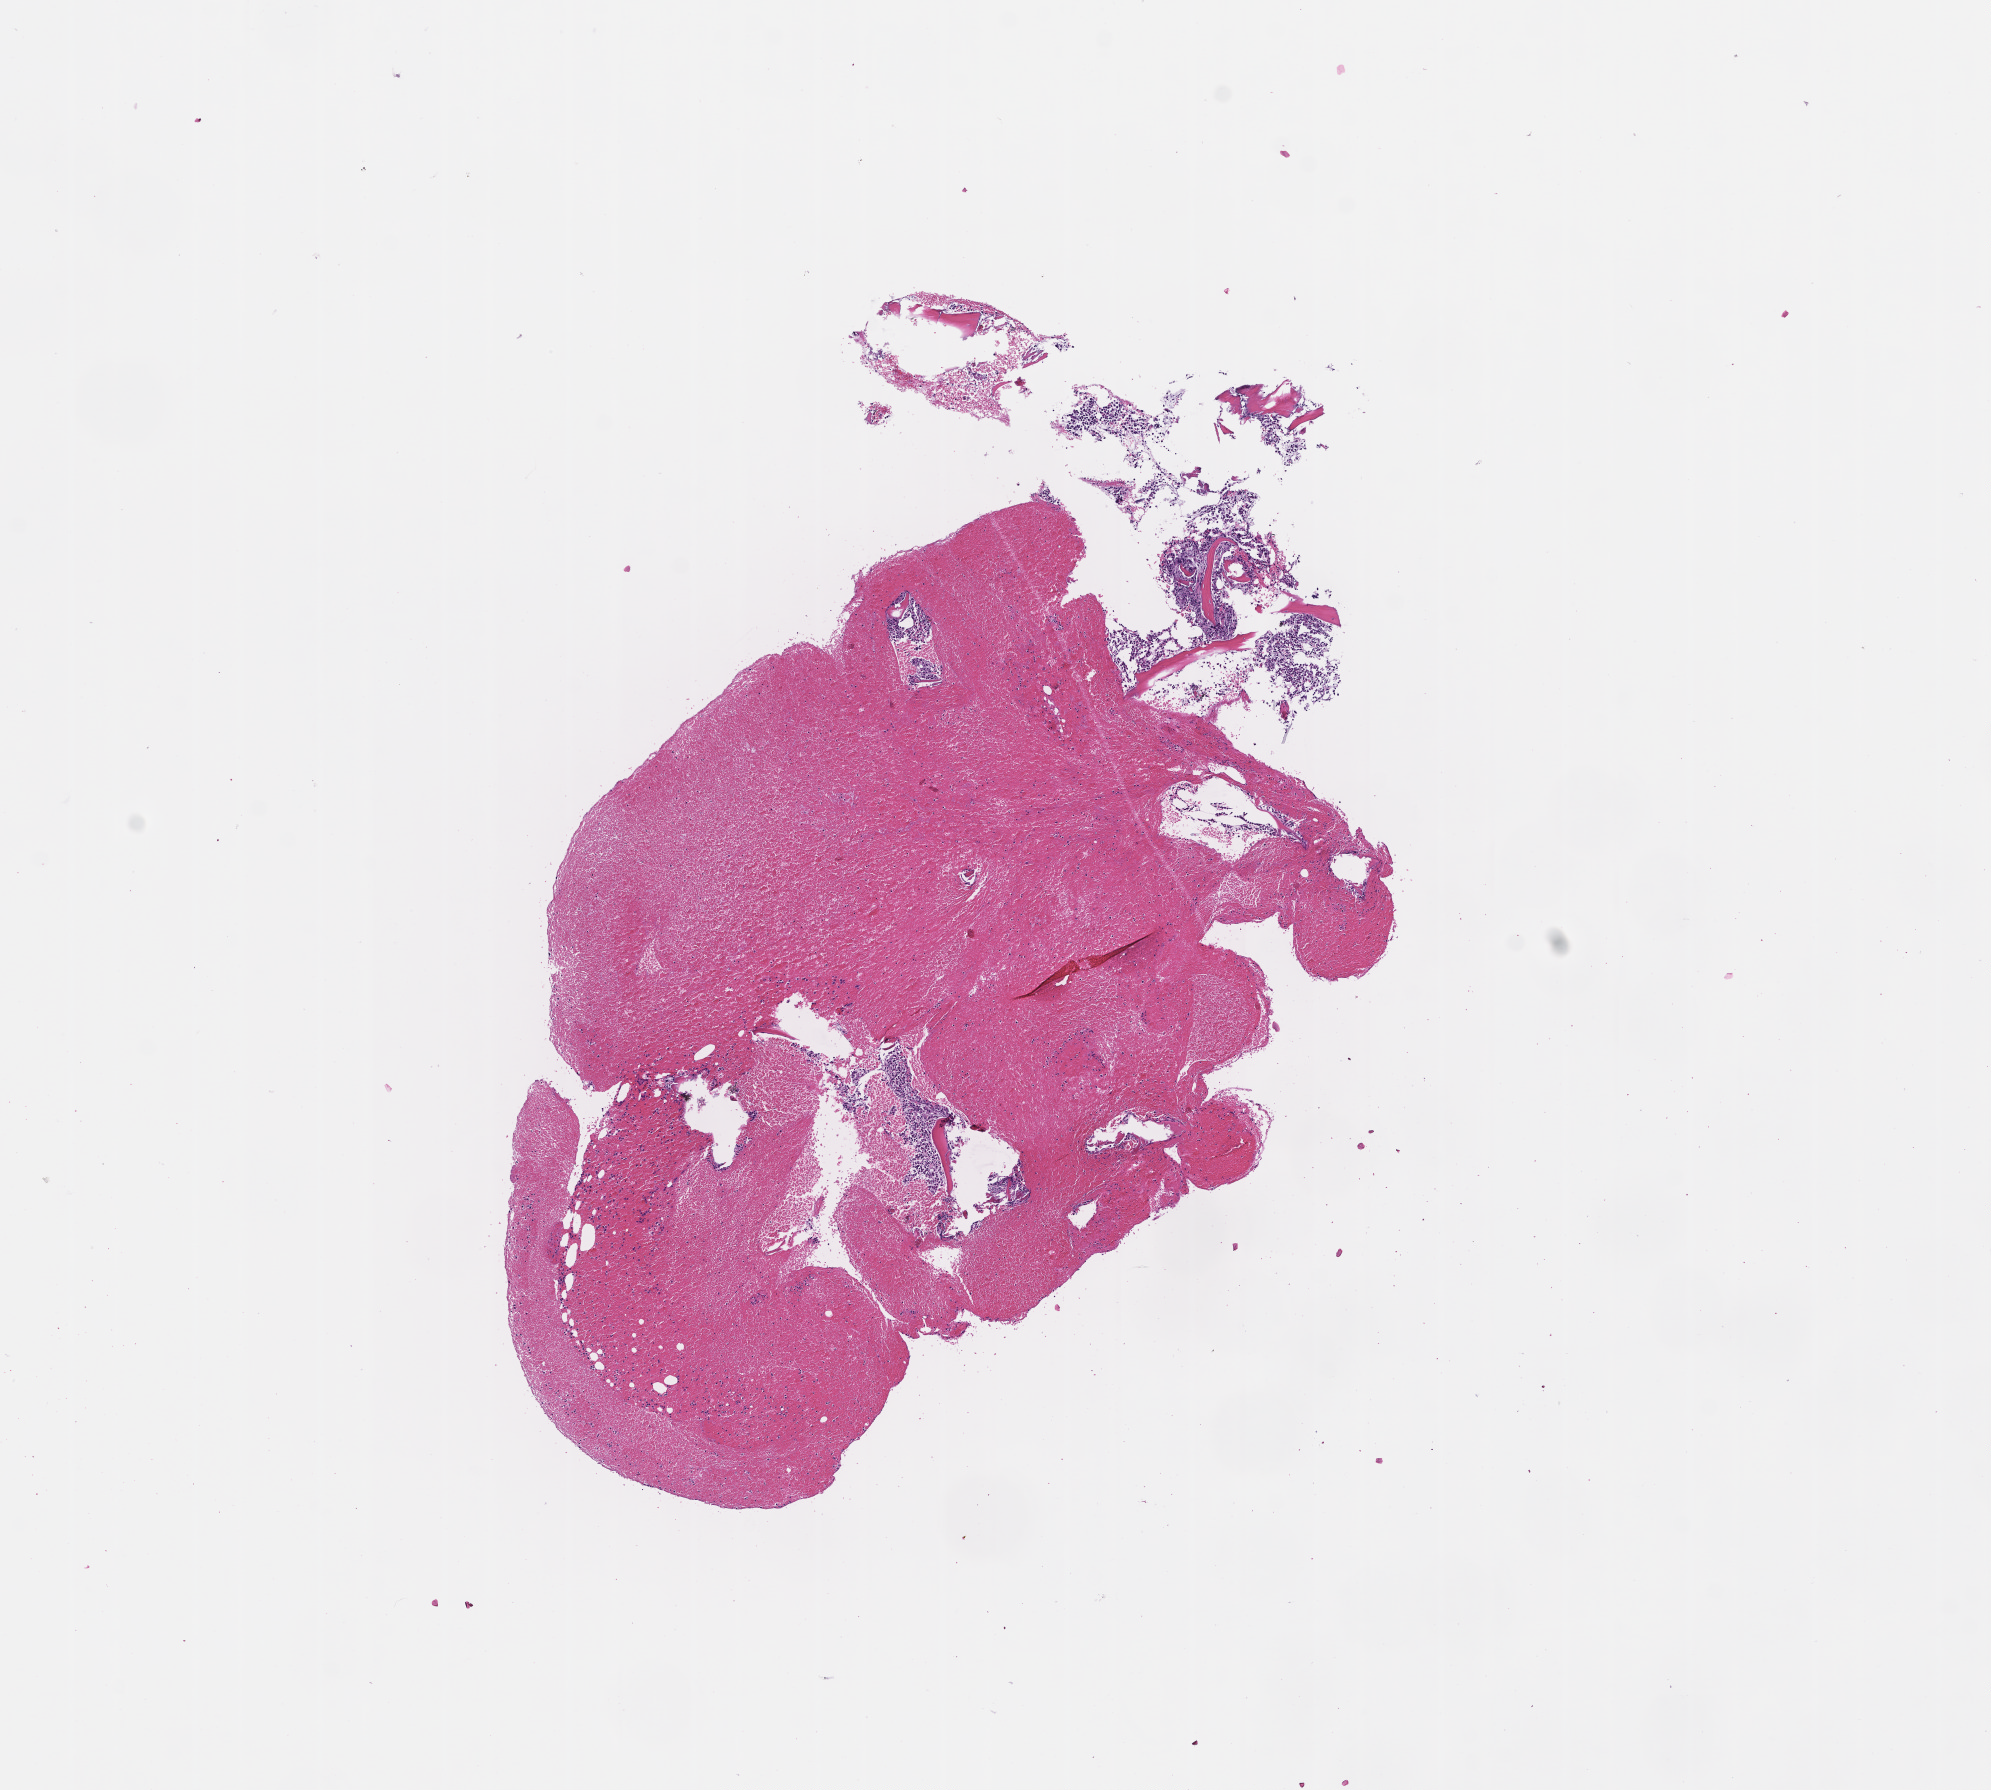
Whole-slide image, haematoxylin and eosin stain — a low-resolution overview of the entire scanned area, about 8.0 x 7.2 mm. Formalin-fixed paraffin-embedded section. Tissue site: bone marrow. Specimen time point: collected at baseline (before treatment). Patient sex: female.
• this section: primary tumour tissue
• diagnosis: Plasma Cell Myeloma